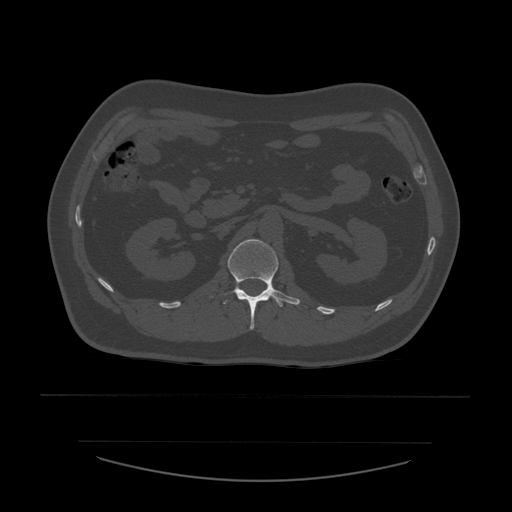
CT including the spine, one axial slice. Slice 224 of 532 in the series (ordered by position). Bone window (W 1800 / L 400 HU). 1.25 mm slice thickness. 512 × 512 image matrix, field of view 441 × 441 mm. Patient age 44 years. Case-level facts recorded for this patient, not image findings: primary cancer: soft tissue sarcoma.
Annotated regions visible in this slice (semi-automatic segmentation, software-assisted and operator-edited):
- L1 vertebra: bounding box (x1, y1, x2, y2) in pixels: (210, 239, 301, 330)